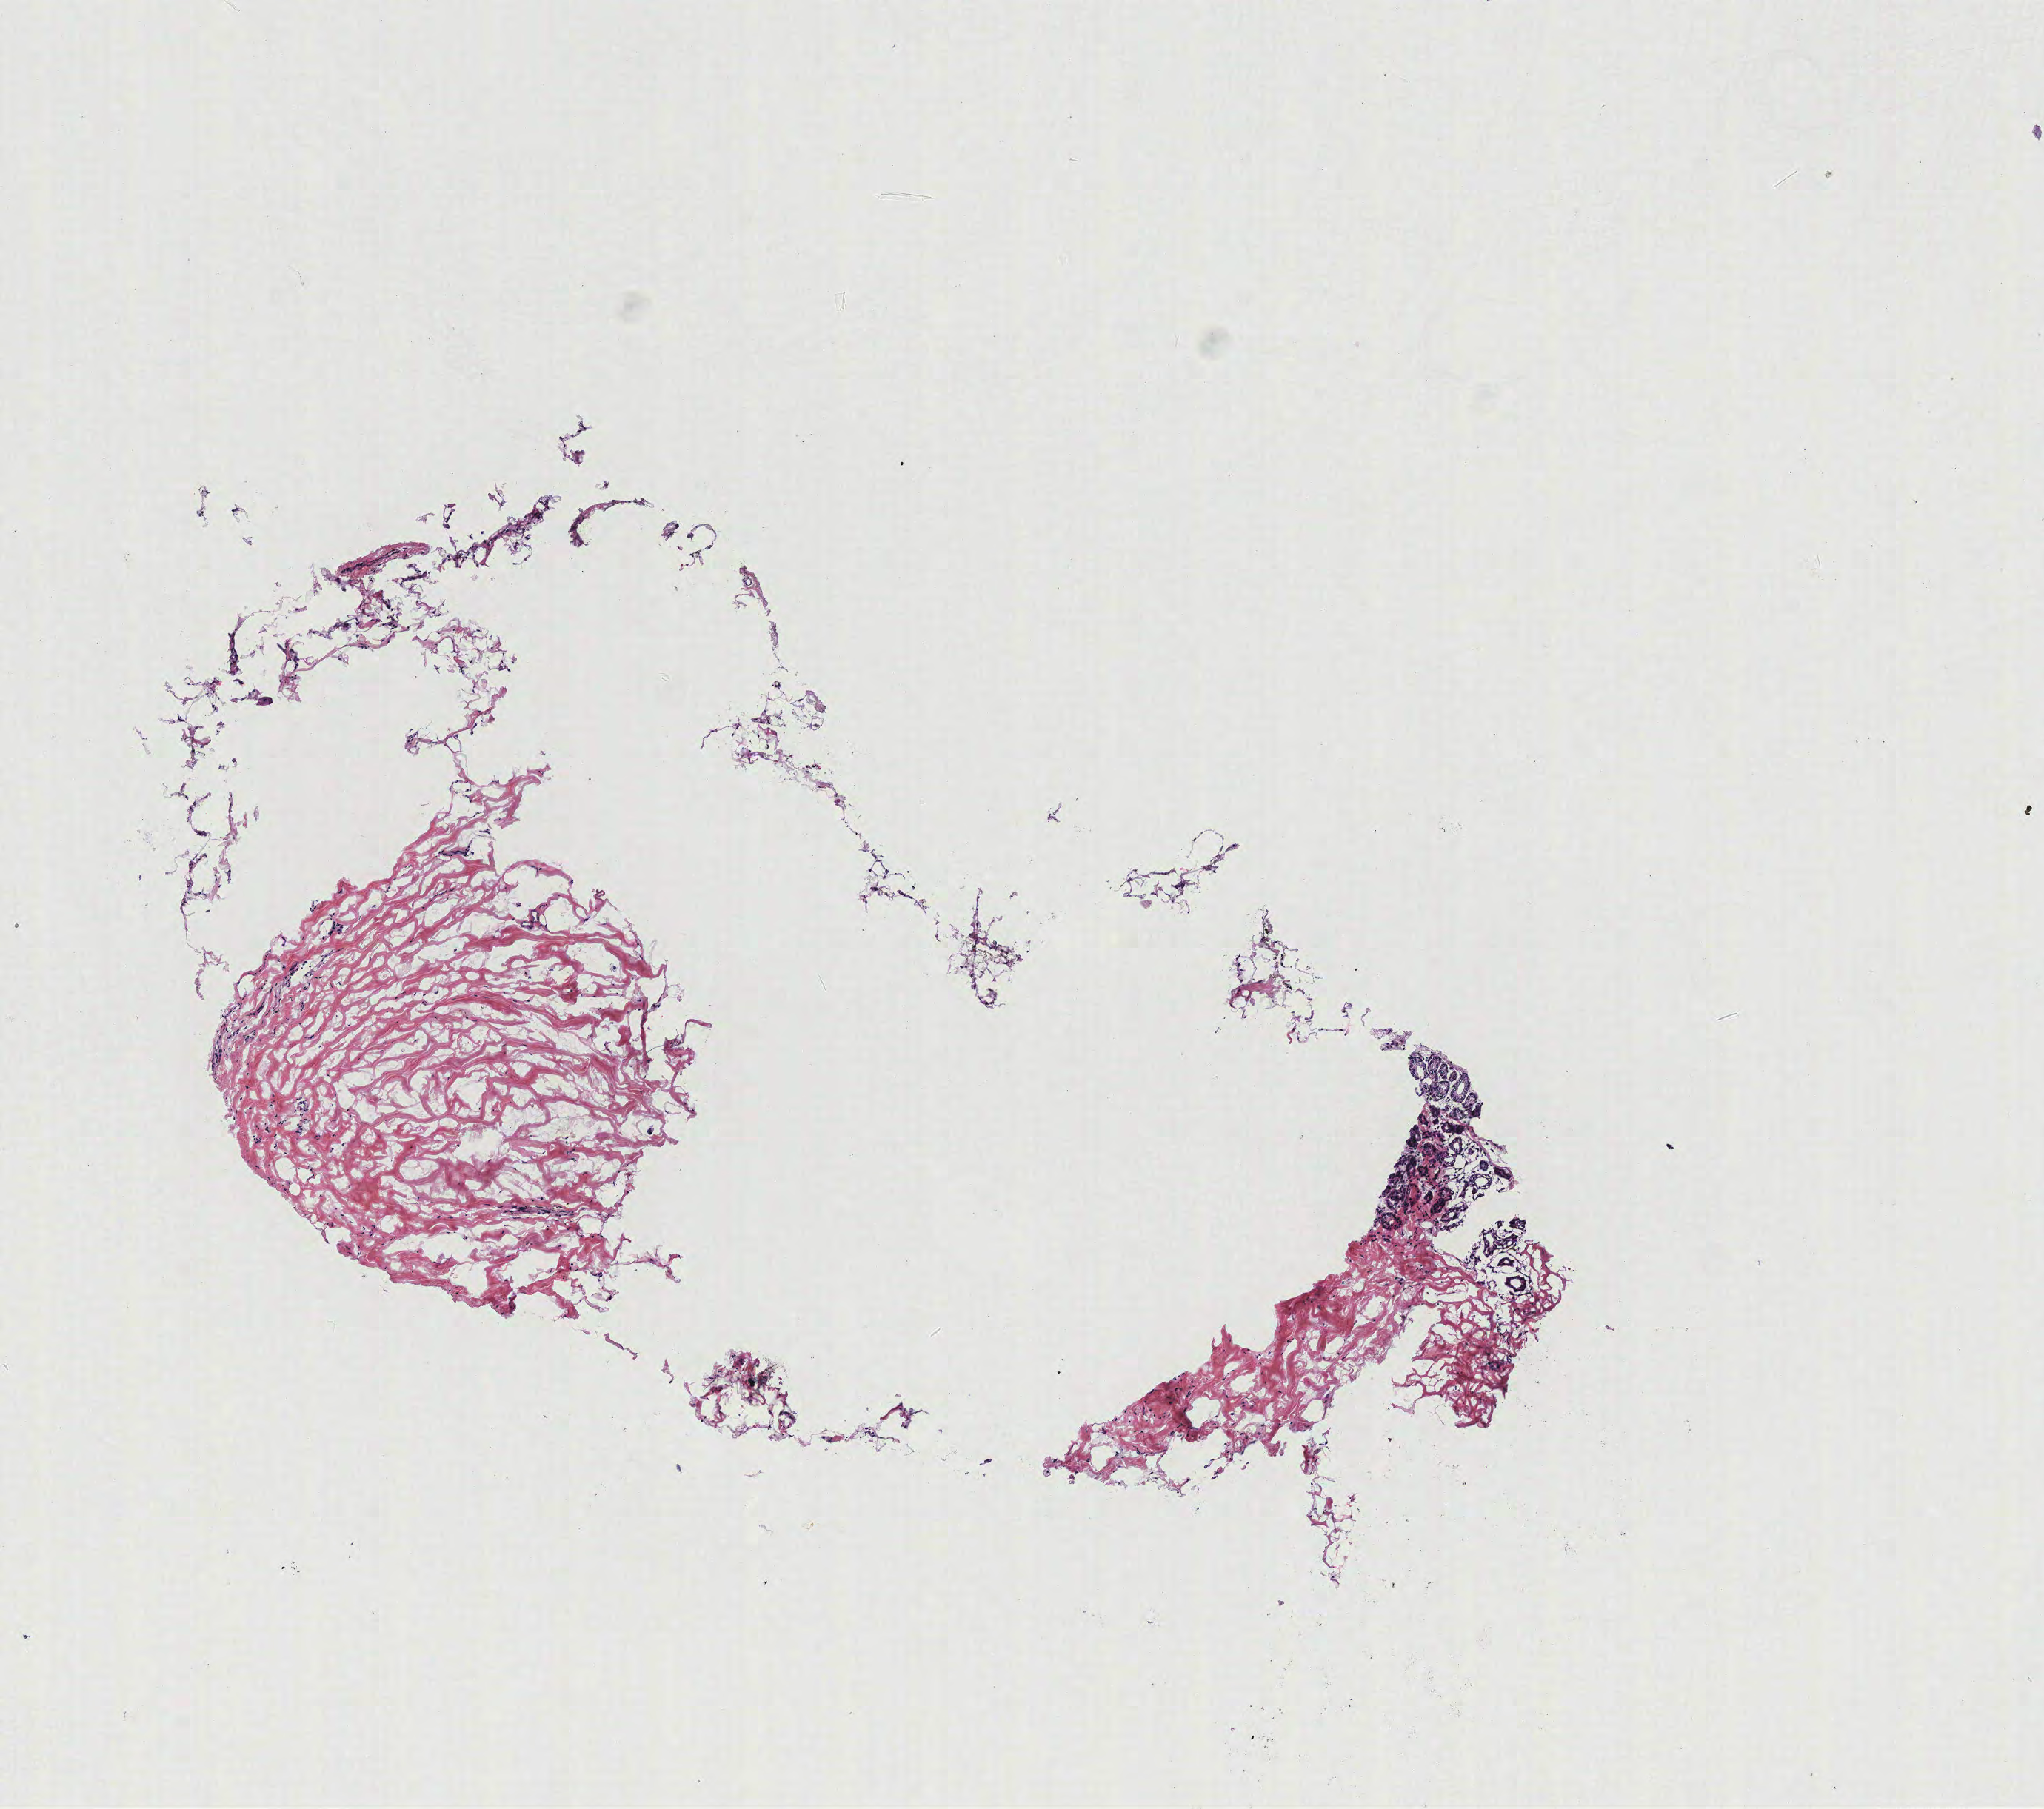
Digitized H&E-stained tissue section (whole slide), whole scanned area (about 5.5 x 4.9 mm) shown as a low-resolution overview, breast, tissue type not recorded. 46-year-old female patient.
Patient diagnosis: Infiltrating duct carcinoma, NOS.